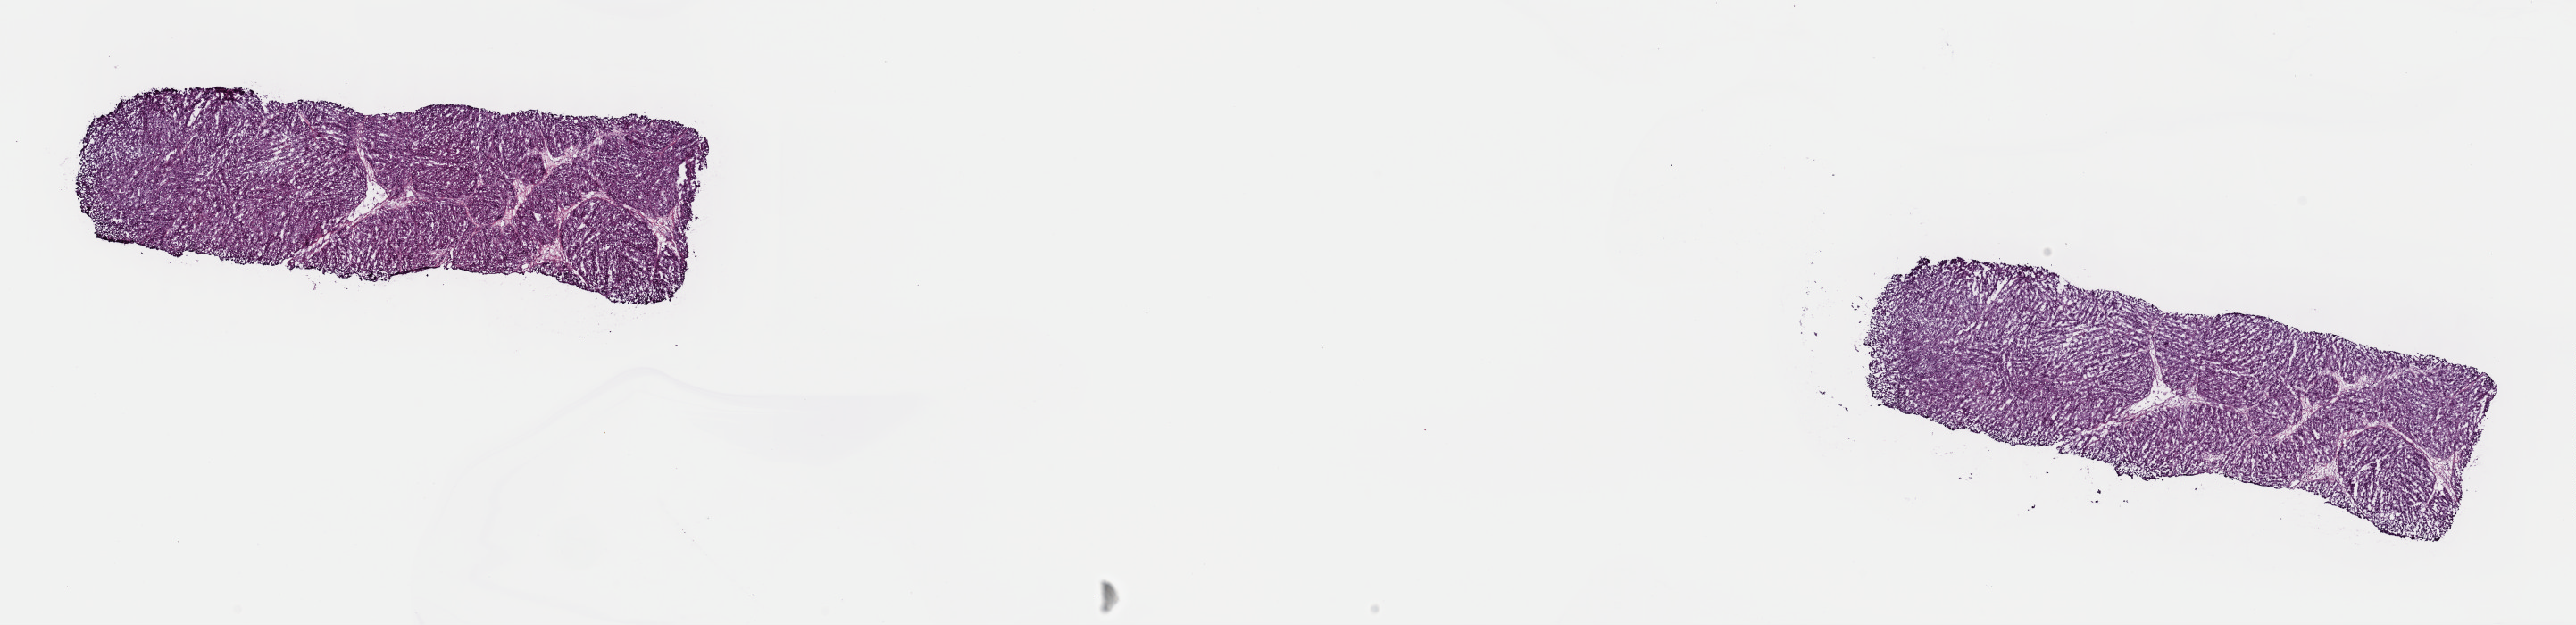
H&E whole-slide image — whole scanned area (about 22.8 x 5.5 mm, acquisition: 40x scan) shown as a low-resolution overview; frozen section; primary tumour sample from the adrenal cortex. Female, age 65 years at initial diagnosis.
Diagnosis: Adrenal cortical carcinoma (cortex of adrenal gland).